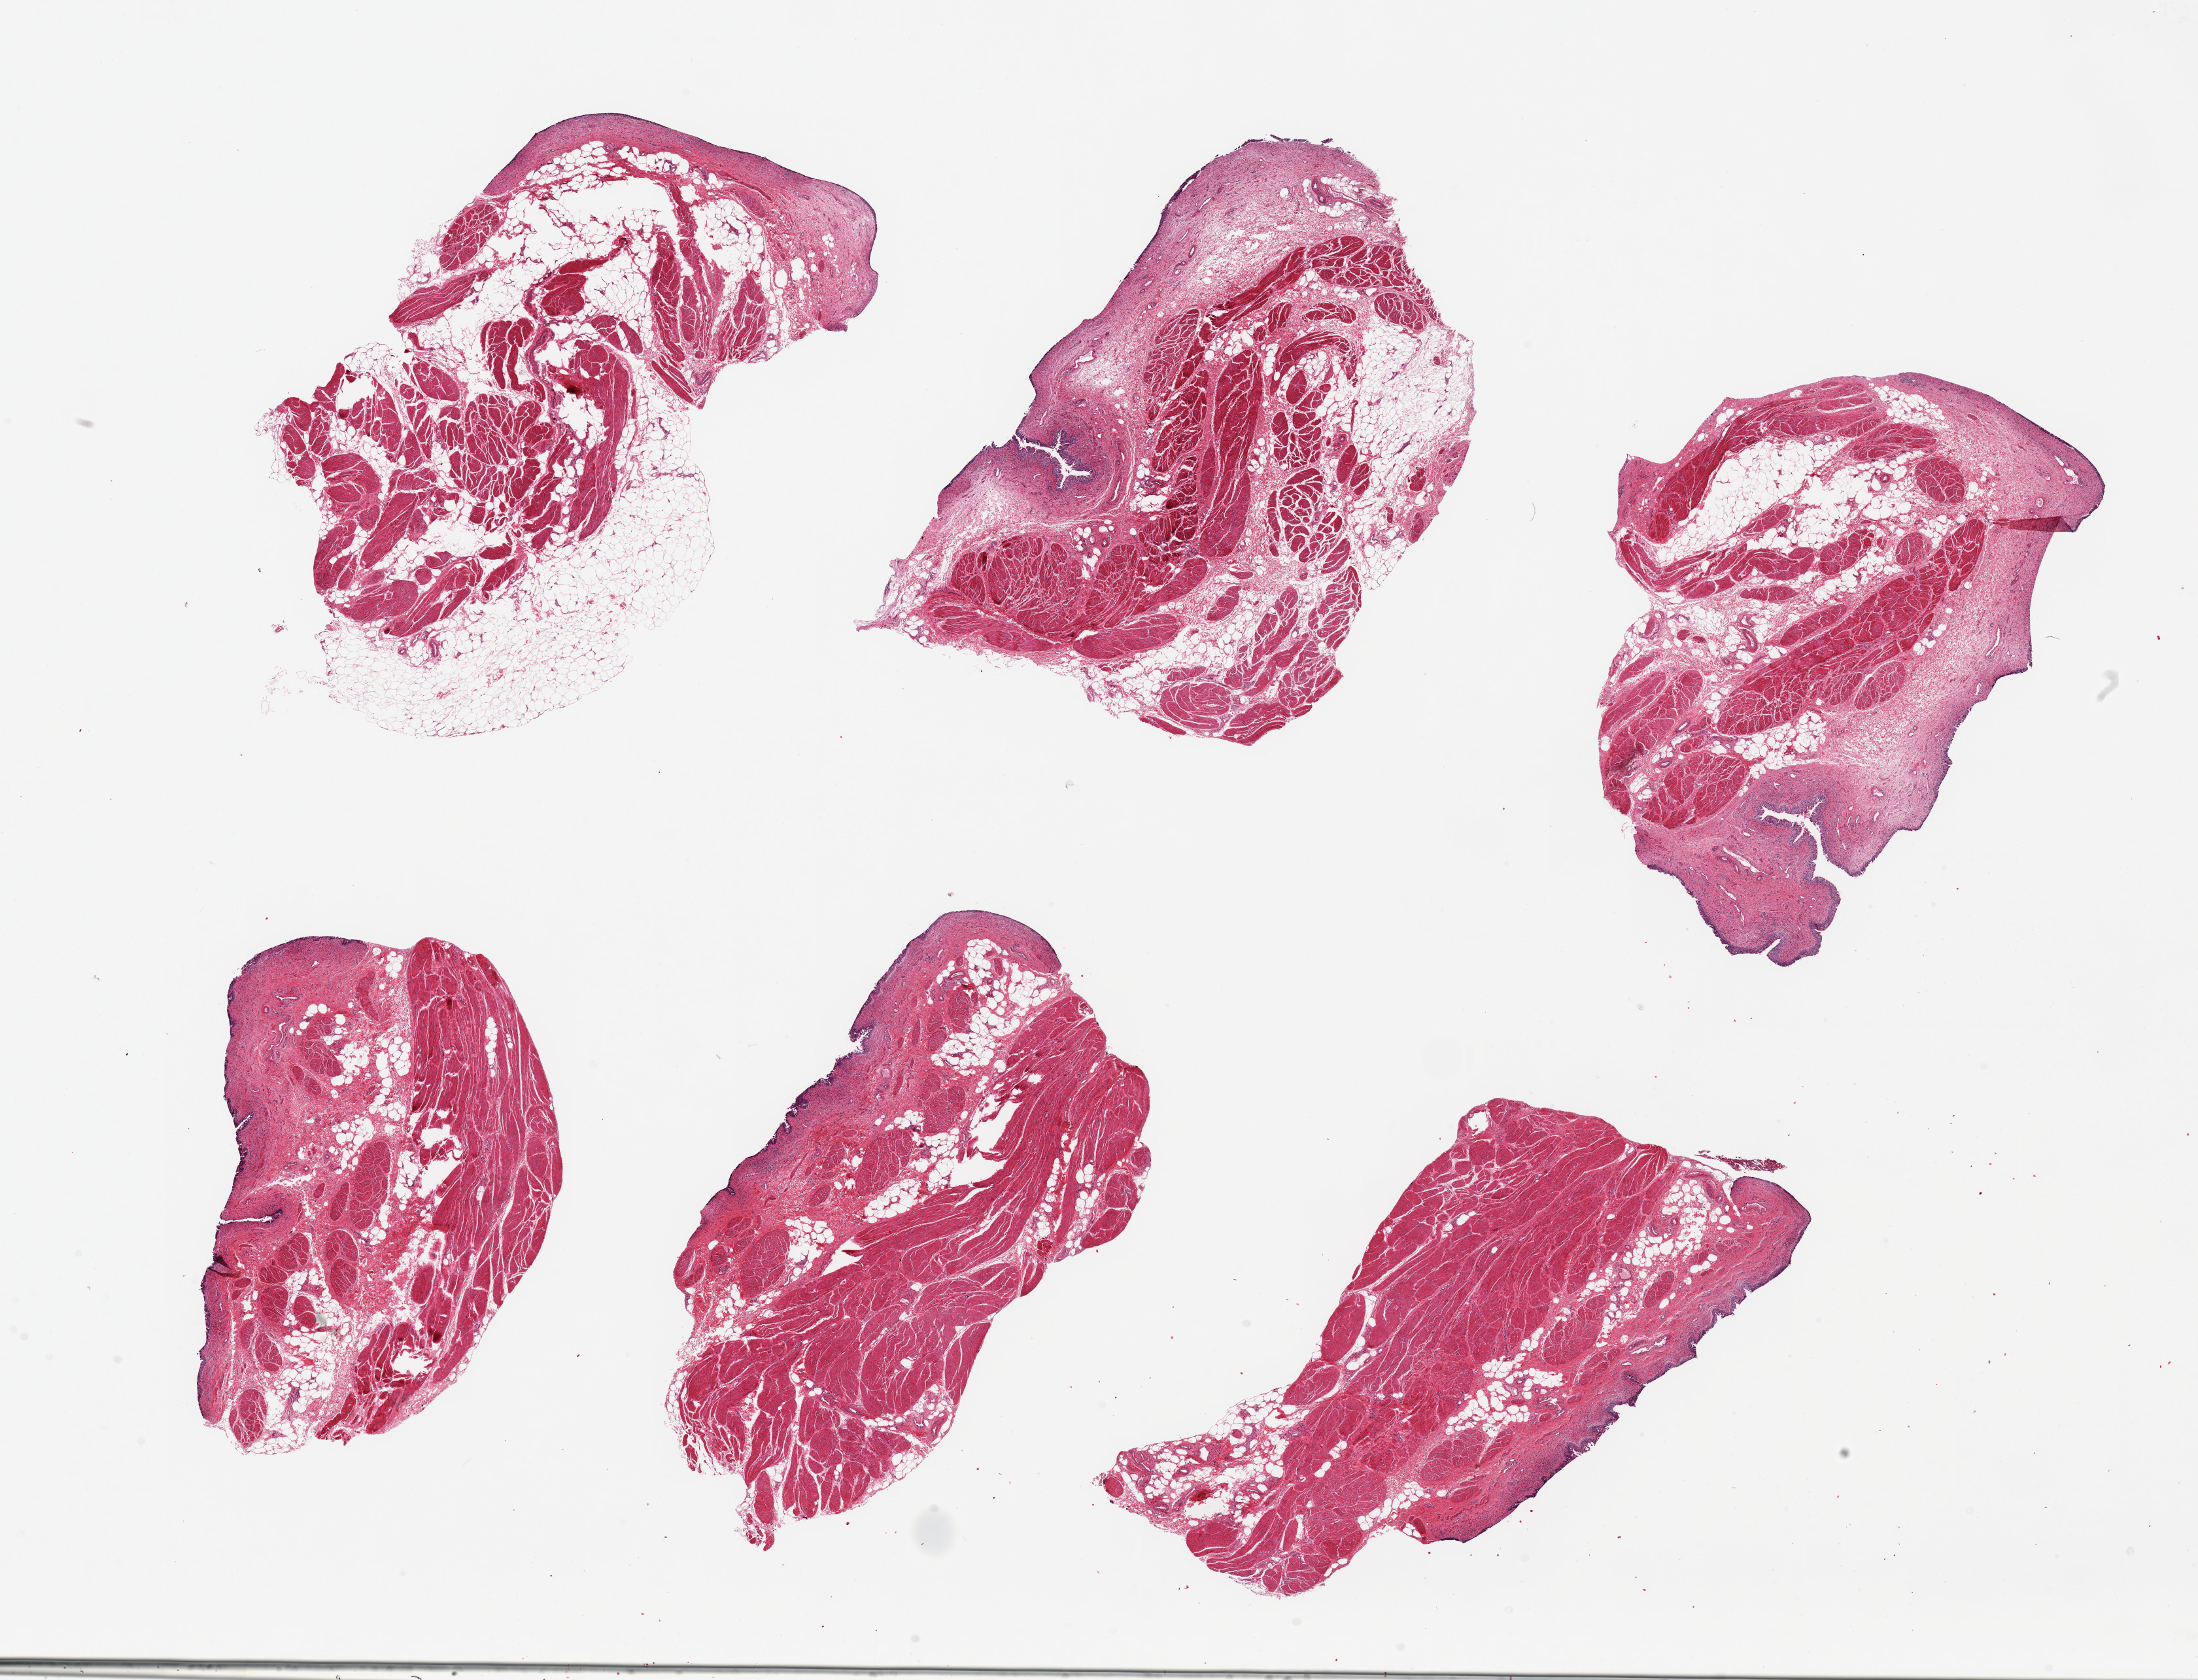
Hematoxylin and eosin (H&E) whole-slide image, brightfield, low-resolution overview of the scanned area, about 26.6 x 20.3 mm (from a 20x scan). PAXgene-fixed paraffin-embedded (PFPE) section. Section of urinary bladder (target tissue). Donor tissue sample. Male donor.
Review note (as recorded): 6 pieces ~7x5mm. Urothelium largely sloughed; a few residual foci up to ~80 microns thick.